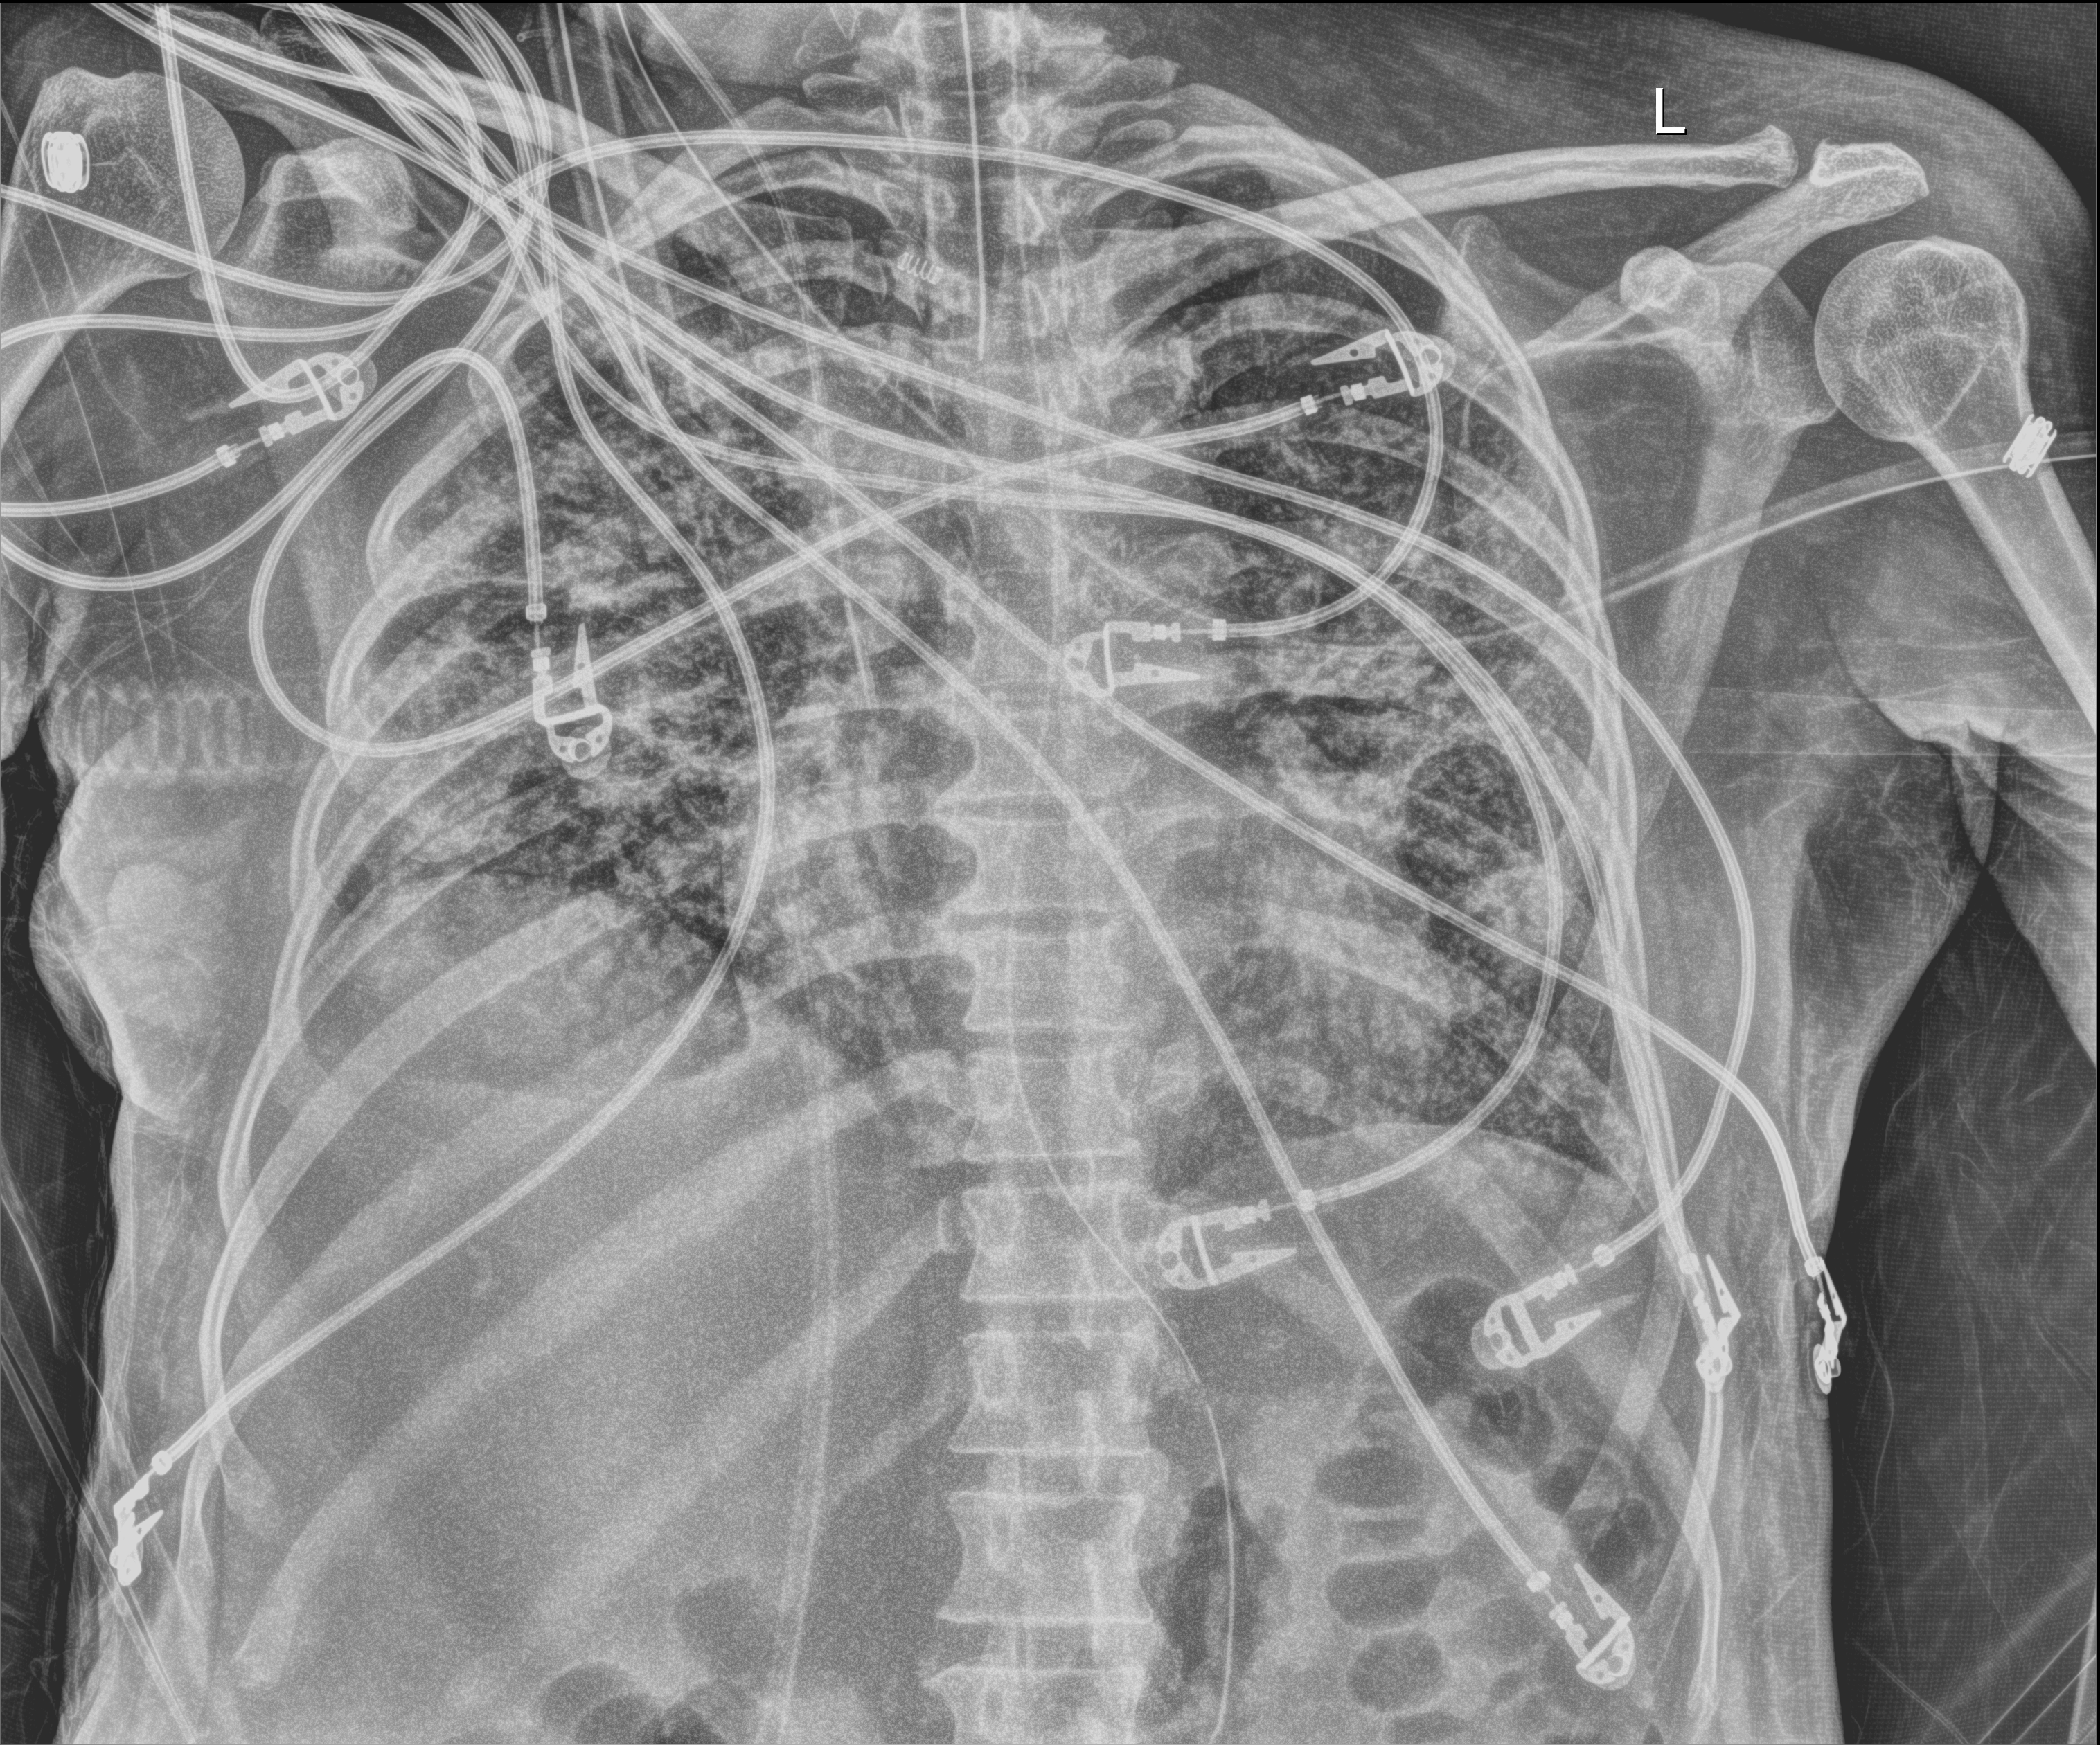
Chest X-ray (portable). Patient hospitalised with COVID-19; female, aged 18–59 years.
Hospital-stay facts (about this admission, not read from this image; timing relative to this image not recorded):
- COPD (admission record): no
- mechanically ventilated during this hospital stay: yes
- chronic kidney disease (admission record): no